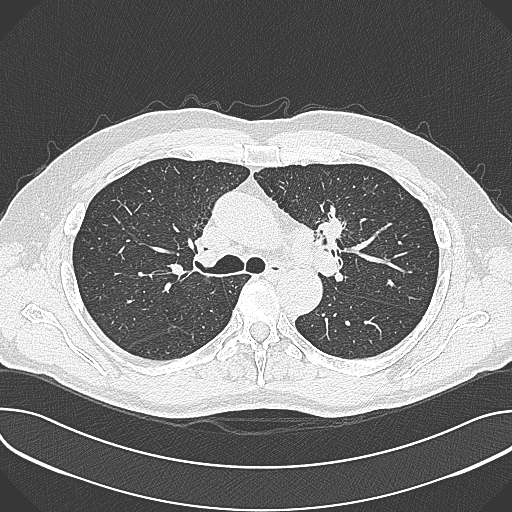
Chest CT (low-dose screening protocol), one axial image. First (baseline) screen. Lung window (W 1500 / L -600 HU). 1 mm slice thickness. Slice 112 of 361 in the series. 512 × 512 image matrix, field of view 380 × 380 mm. Male, age 59 years at enrolment.
• Expert reader's lesion annotation, bounding box [x1, y1, x2, y2] px = [303, 194, 364, 257].
• The screening reader recorded 2 non-calcified nodules or masses ≥4 mm on this exam (left upper lobe, left upper lobe); which of them this box marks is not recorded.
• Lung cancer was diagnosed 21 days after this screen: non-small cell carcinoma, left upper lobe, poorly differentiated (G3), stage IIIA (AJCC 6th edition), 35 mm at pathology.